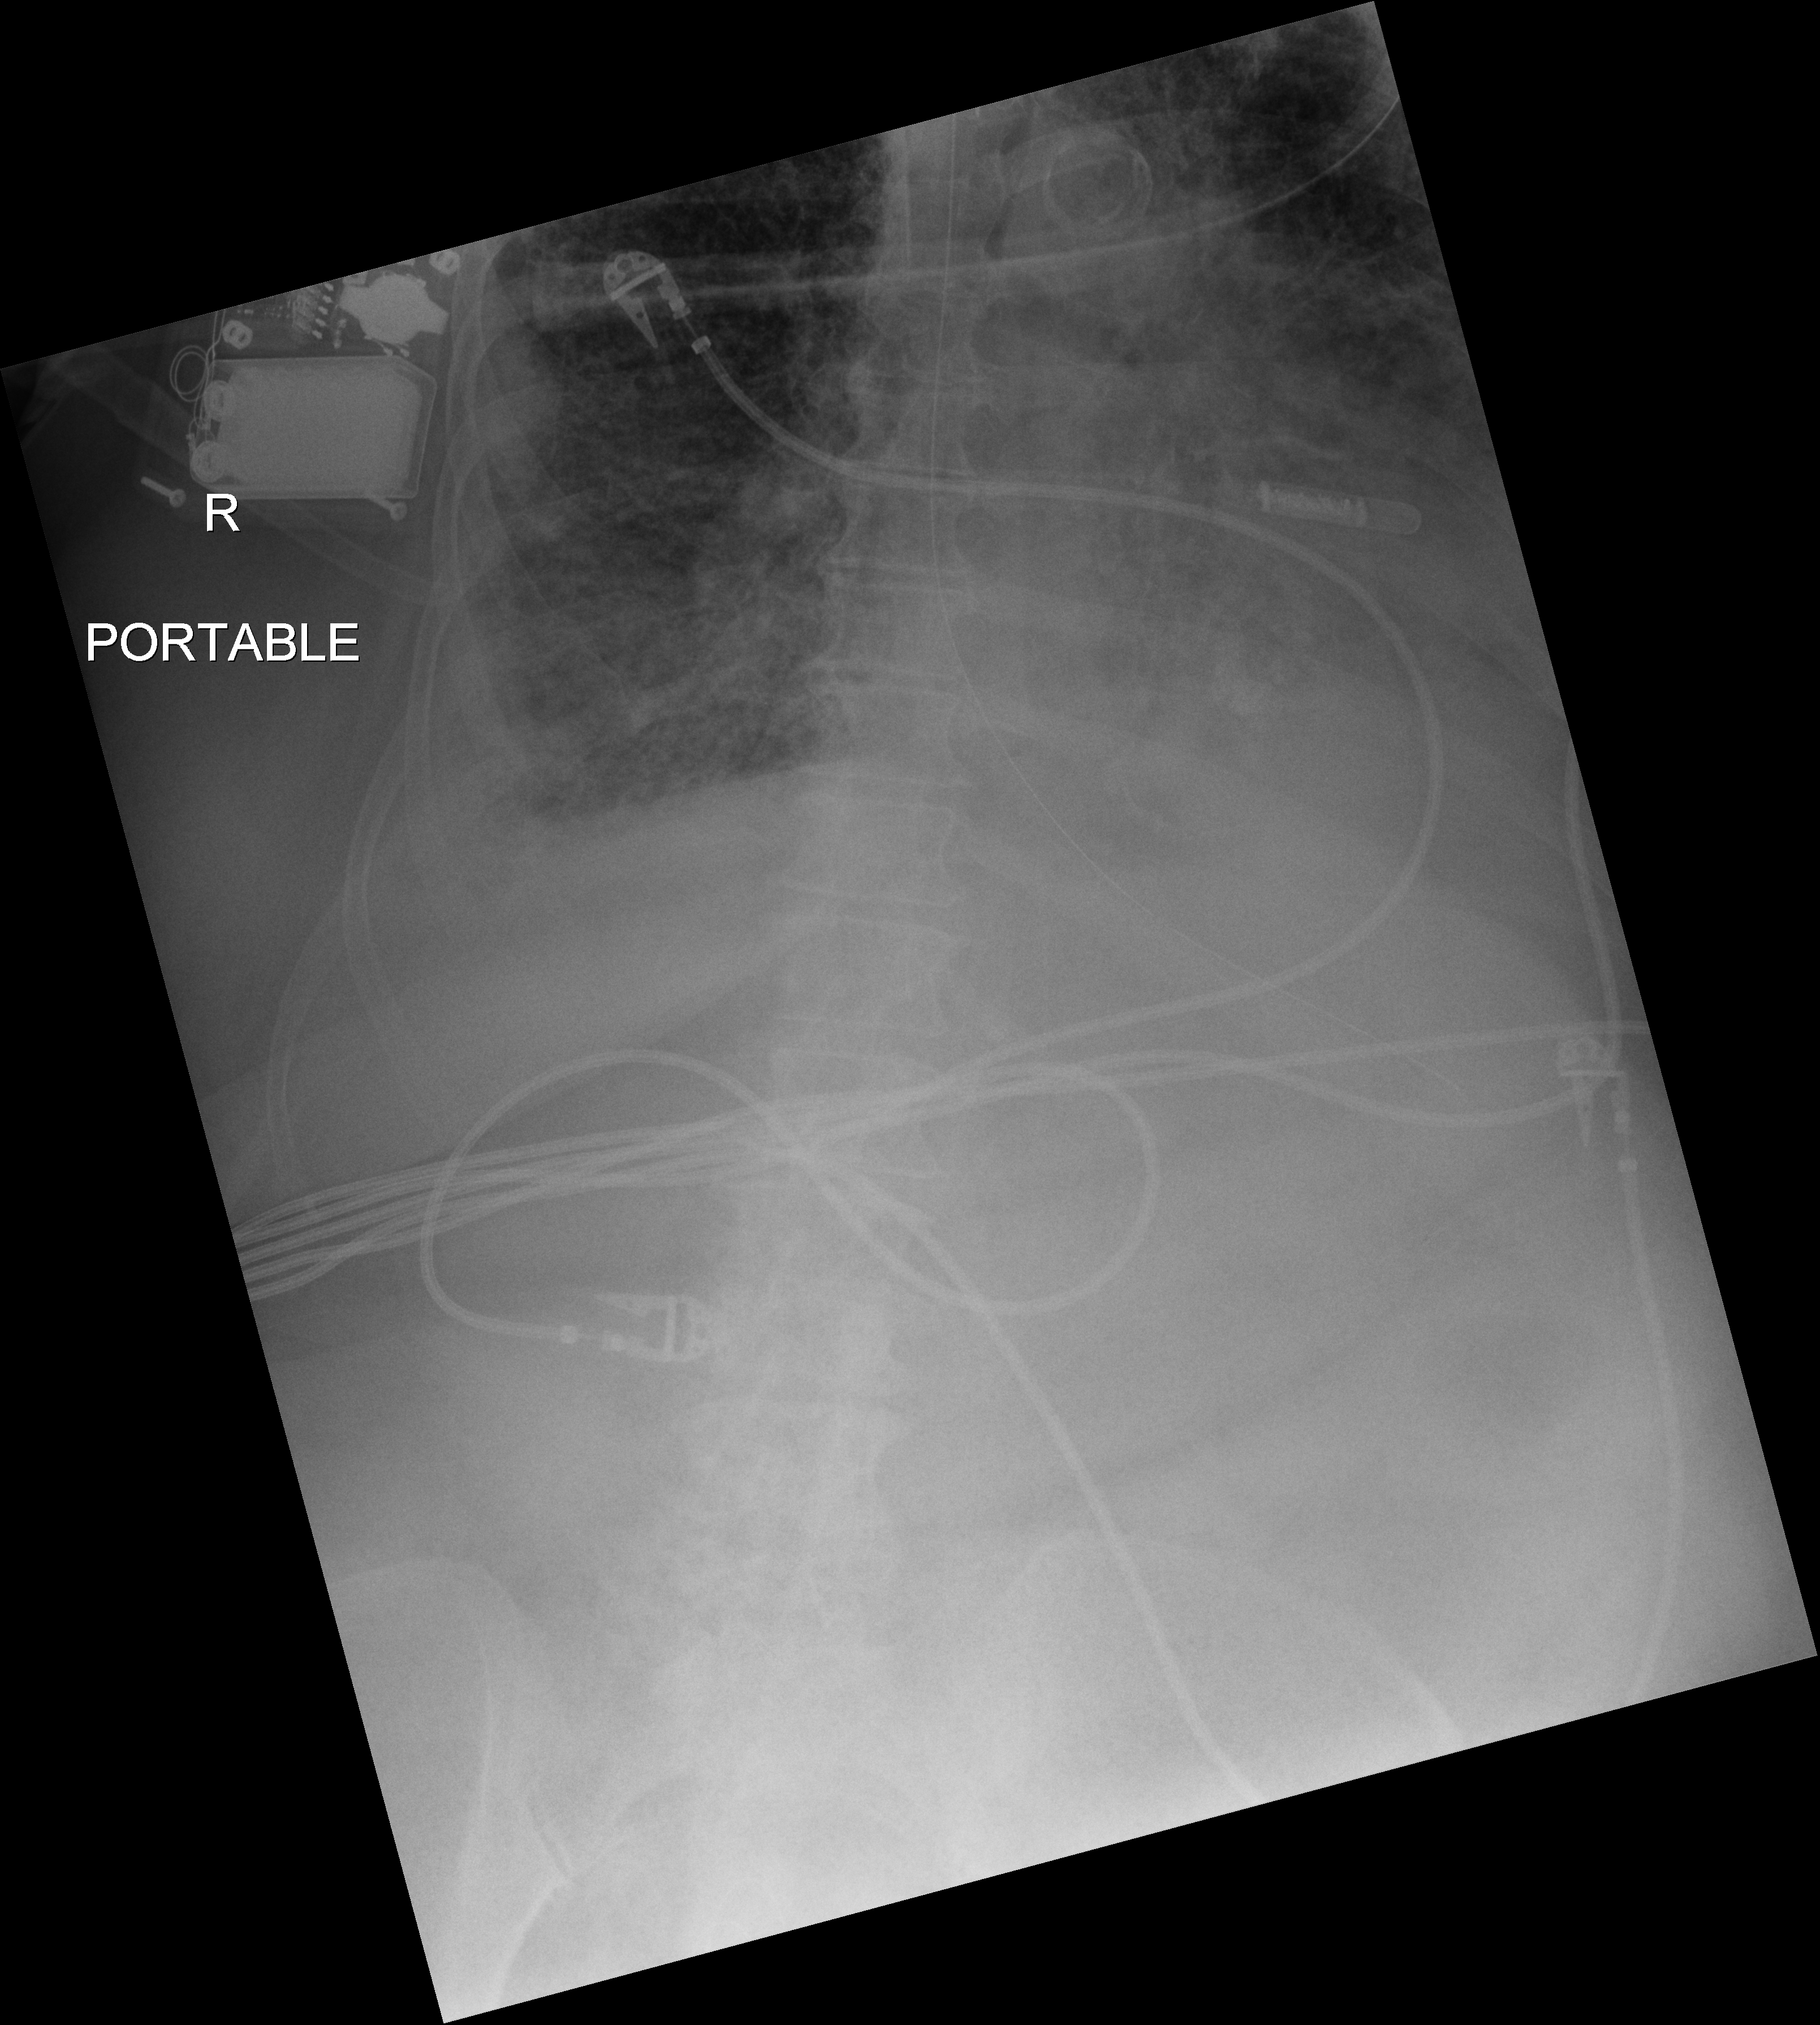
Portable chest radiograph, anteroposterior (AP) projection. Female patient hospitalised with COVID-19, age 60–74 years.
From the hospital-stay record, not from the radiograph (when in the stay this image was taken is not recorded):
- mechanically ventilated during this hospital stay: yes
- length of hospital stay: 28 days
- admitted to intensive care during this hospital stay: yes